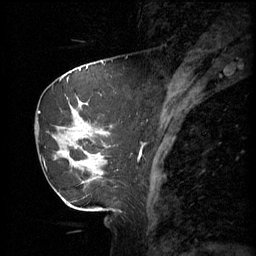
Breast MRI (dynamic contrast-enhanced), one sagittal slice. Slice 19 of 60 in the series (ordered by position). 3 images stored at this slice position (order not interpretable as contrast timing). 1.5 T. TE 4.2 ms, TR 11 ms. 2 mm slice thickness. 256 × 256 image matrix, field of view 220 × 220 mm. Patient: female, 69 years.
Annotated regions visible in this slice (semi-automatic segmentation, software-assisted and operator-edited):
- analysis volume of interest (the breast-tissue region the enhancement analysis was run in; not a lesion): bounding box <38,88,115,189> (left, top, right, bottom; pixels)
- tumour enhancement mask (voxels above the 70 % enhancement threshold inside the analysis volume of interest): <57,100,103,183>